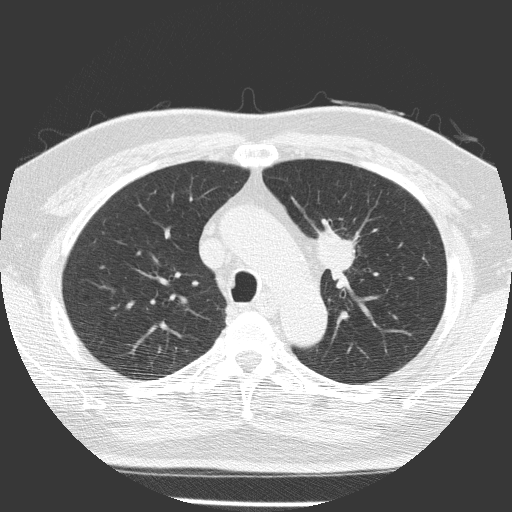
Low-dose screening chest CT, one axial slice. Slice 110 of 156 in the series (ordered by position). 120 kVp. Lung window (W 1500 / L -600 HU). 512 × 512 image matrix, field of view 309 × 309 mm.
Outlined on this slice (manually delineated by an expert):
- lesion 1 (tumor, upper lobe of left lung): bounding box <318,228,355,281> (left, top, right, bottom; pixels)